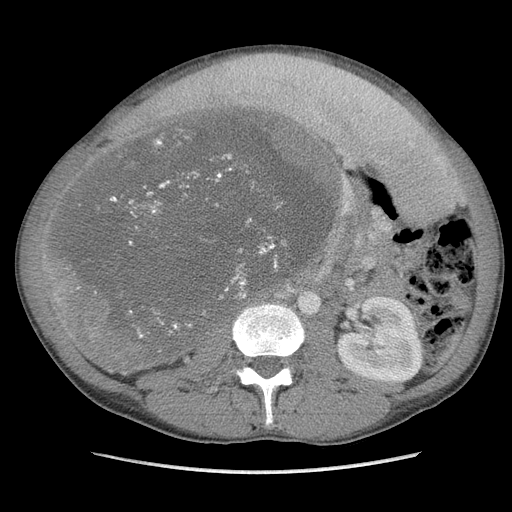
Contrast-enhanced abdominal CT, one axial slice; position 55 of 115 along the scan axis; soft-tissue window (W 400 / L 40 HU); 5 mm slice thickness; 512 × 512 image matrix, field of view 360 × 360 mm. Male patient. From the clinical record (not read from this slice): diagnosis: adrenocortical carcinoma; tumour side: right adrenal; Ki-67 index: 13 %; stage (as recorded): 3.
Annotated regions visible in this slice (semi-automatically segmented with operator editing):
- mass: bounding box (x1, y1, x2, y2) in pixels: (54, 113, 337, 365)